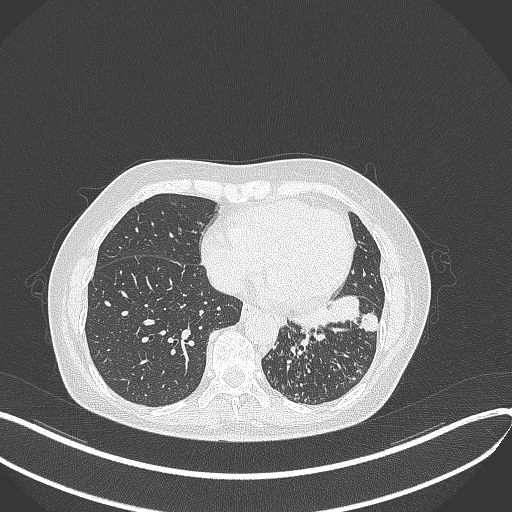
Chest CT, one axial slice; slice 140 of 429 in the series (ordered by position); 100 kVp; lung window (W 1500 / L -600 HU); 1 mm slice thickness; 512 × 512 image matrix, field of view 400 × 400 mm. Patient: female, 63 years. From the clinical record (not read from this slice): clinical TNM (as recorded): T1b N0 M0.
Structures marked on this image (bounding box drawn by a radiologist):
- lung tumour (recorded histology: adenocarcinoma): box from (x=286, y=294) to (x=380, y=339) px